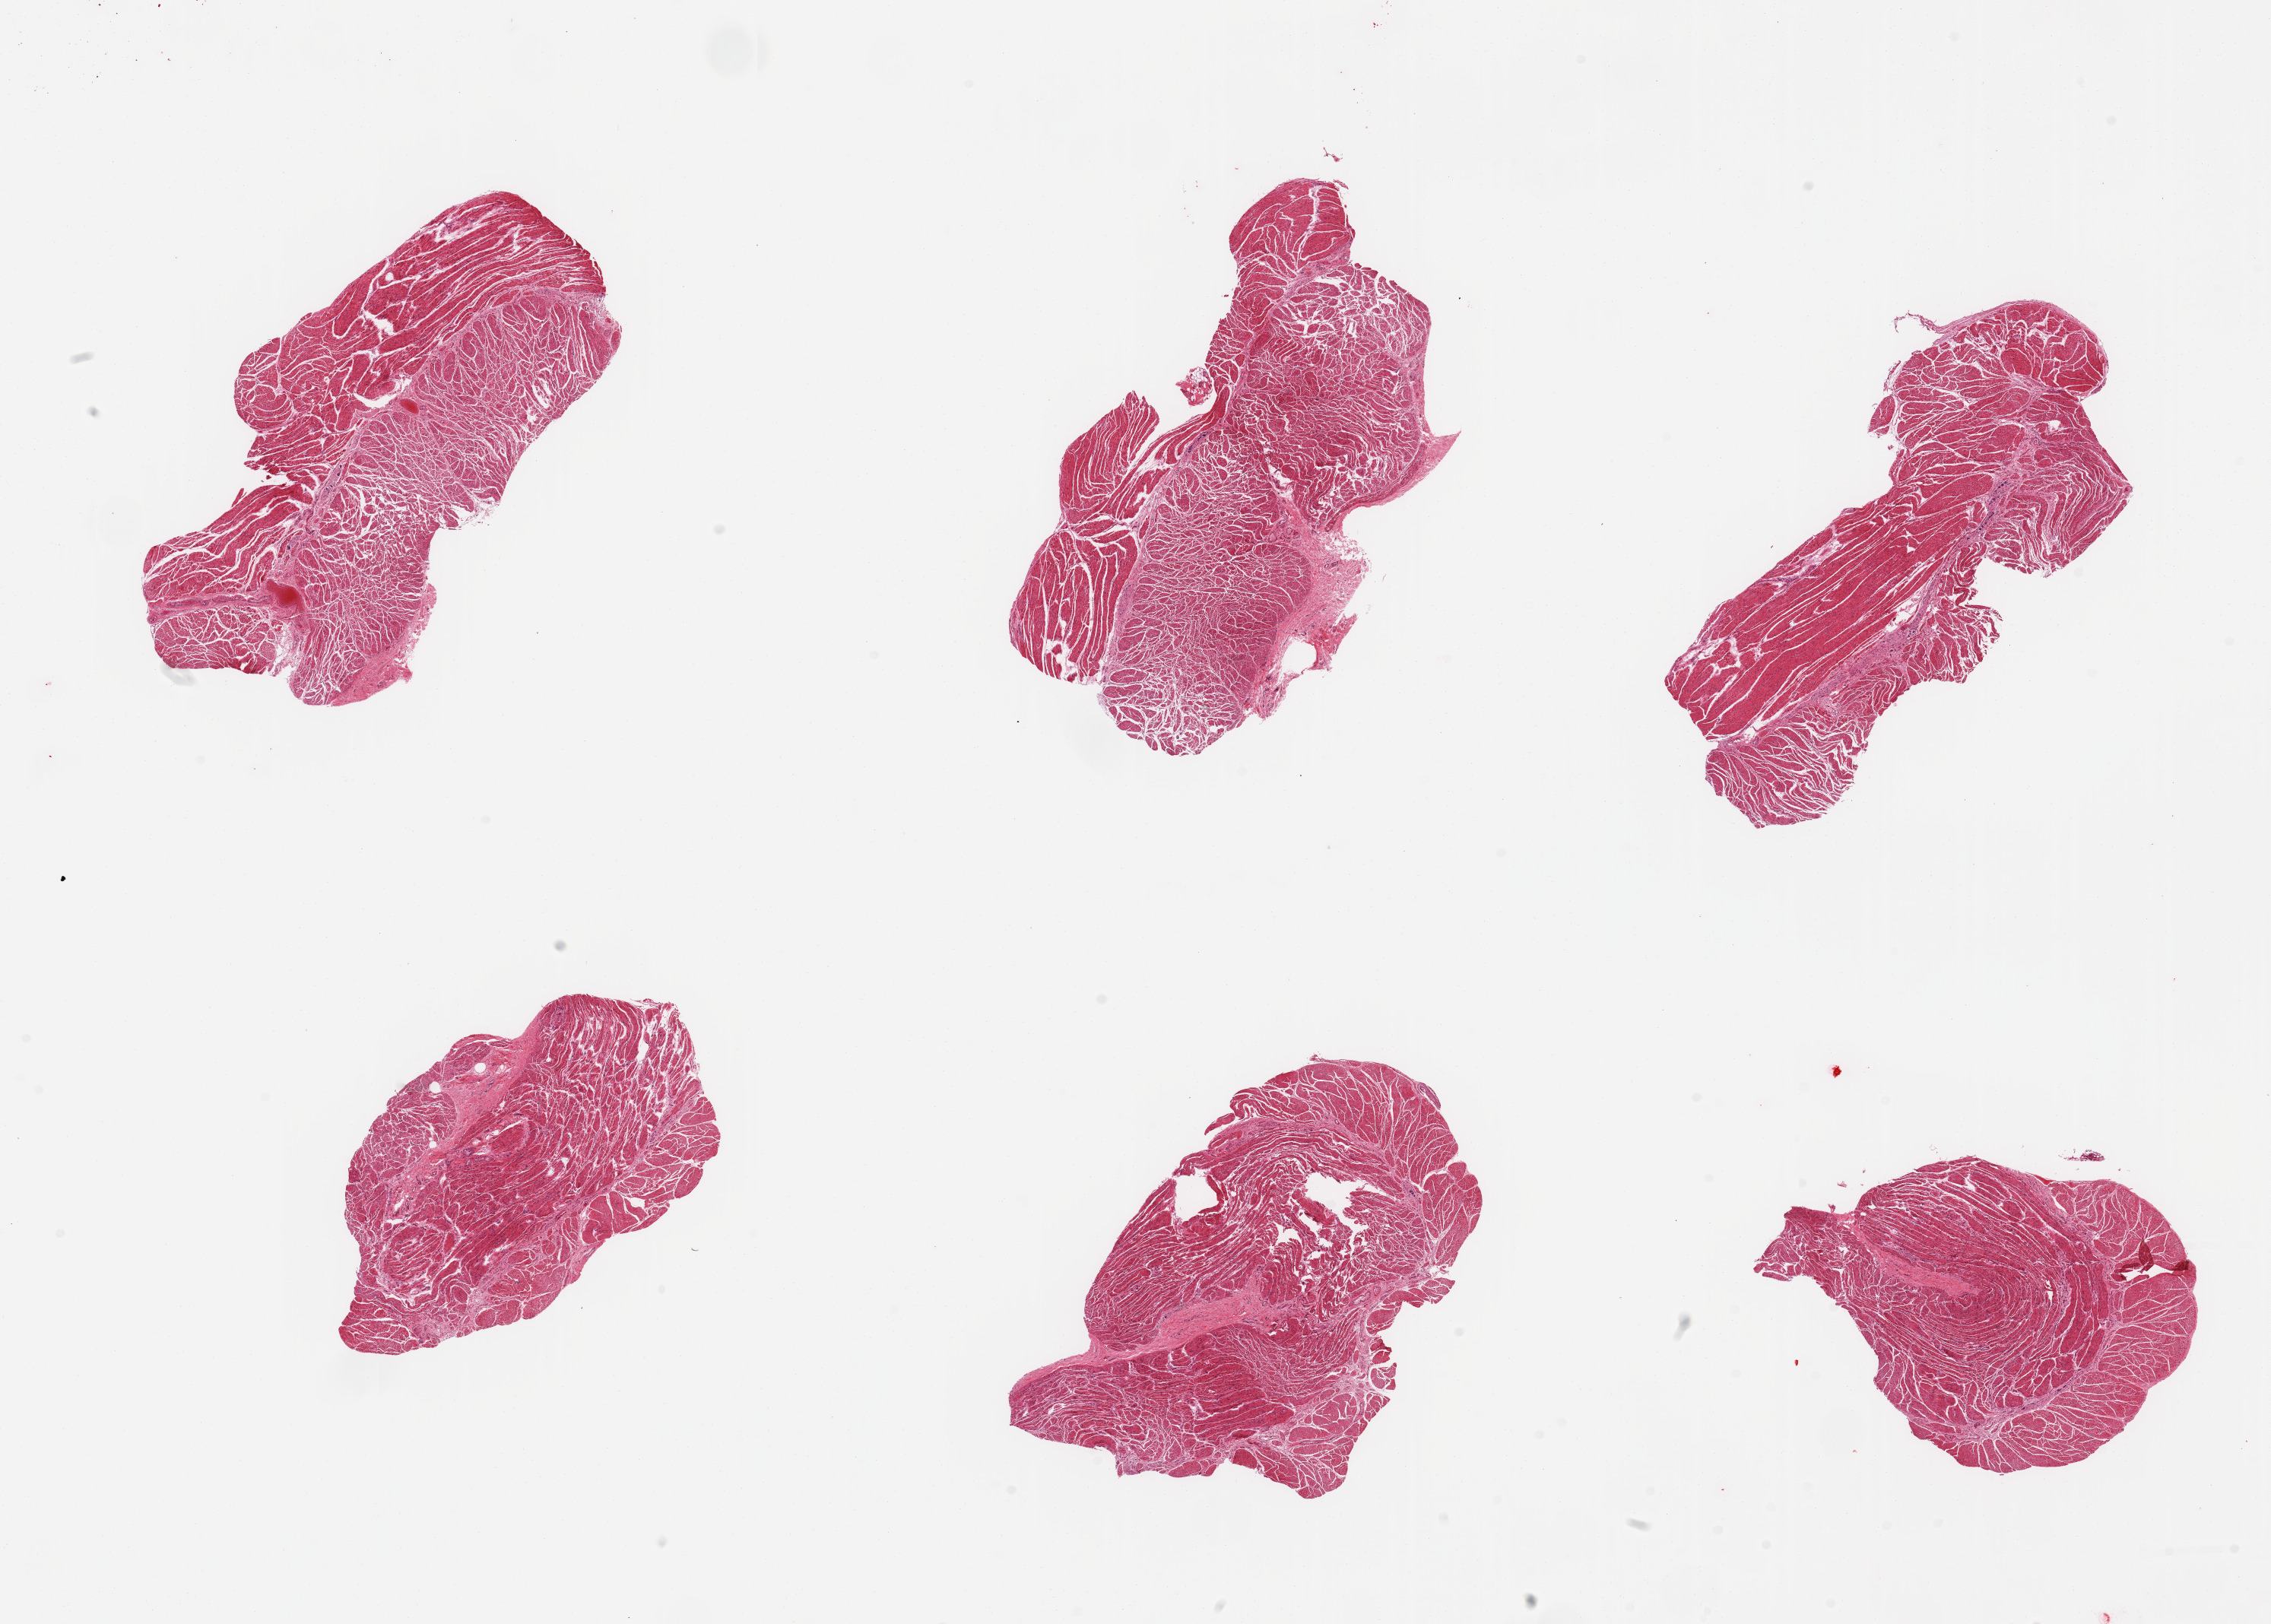
Whole-slide image, H&E stain — a low-resolution overview of the entire scanned area, about 23.6 x 16.9 mm. PAXgene-fixed, paraffin-embedded tissue. Target tissue: esophageal muscle. Donor tissue sample. Male donor.
Reviewer comment on this tissue sample: 6 pieces; well dissected muscle.